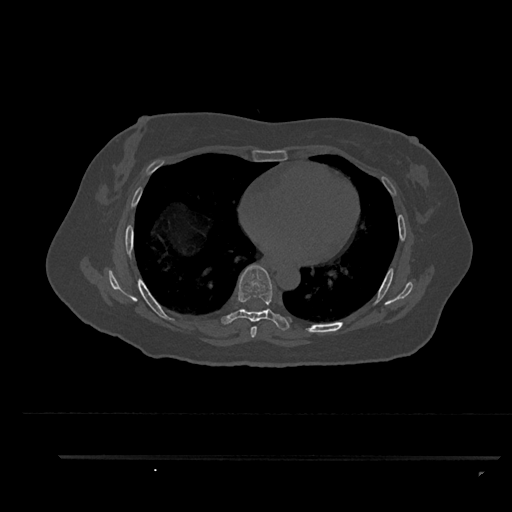
CT including the spine, one axial slice. Slice 512 of 797 in the series (ordered by position). Bone window (W 1800 / L 400 HU). 512 × 512 image matrix, field of view 408 × 408 mm. Female patient, age 44 years. From the clinical record (not read from this slice): primary cancer: renal; vertebrae with lytic lesions (as recorded): L1.
Annotated regions visible in this slice (semi-automatically segmented with operator editing):
- T6 vertebra: bounding box (x1, y1, x2, y2) in pixels: (250, 326, 257, 338)
- T7 vertebra: (221, 265, 291, 331)